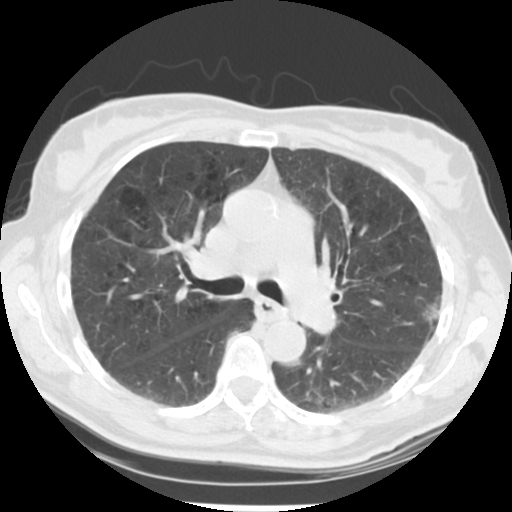
Low-dose screening chest CT, one axial slice. Position 136 of 223 along the scan axis. Reconstruction kernel STANDARD. 120 kVp. Lung window (W 1500 / L -600 HU). 512 × 512 image matrix, field of view 302 × 302 mm.
Annotated regions visible in this slice (expert manual segmentation):
- lesion 1 (tumor, upper lobe of left lung): bounding box <423,303,440,325> (left, top, right, bottom; pixels)